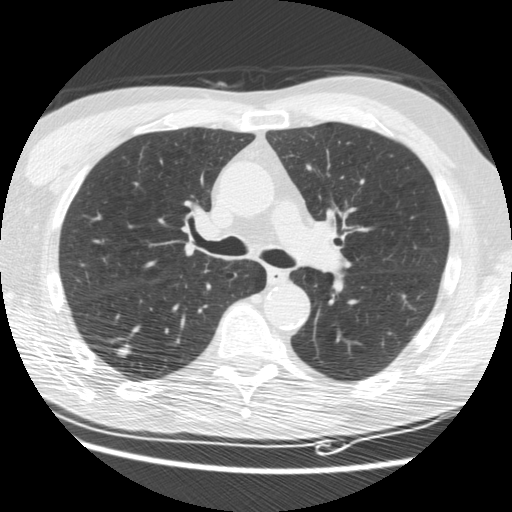
Low-dose screening chest CT, one axial slice; position 108 of 176 along the scan axis; reconstruction kernel STANDARD; lung window (W 1500 / L -600 HU); 2.5 mm slice thickness; 512 × 512 image matrix, field of view 347 × 347 mm.
Annotated regions visible in this slice (expert manual segmentation):
- lesion 1 (tumor, lower lobe of right lung): bounding box <117,348,131,357> (left, top, right, bottom; pixels)